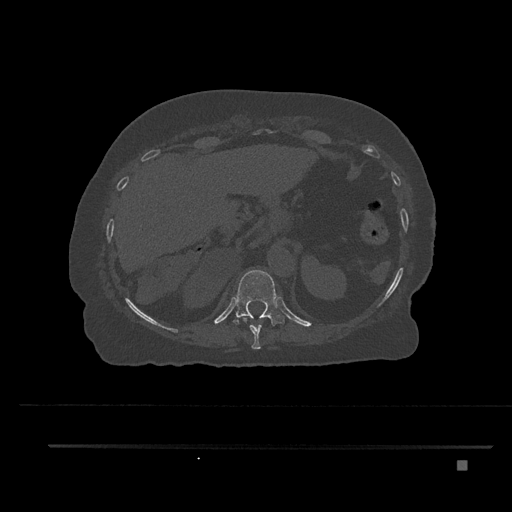
CT including the spine, one axial slice; reconstruction kernel Br40s/3; 120 kVp; bone window (W 1800 / L 400 HU); 512 × 512 image matrix, field of view 437 × 437 mm. Patient: female, 76 years. From the clinical record (not read from this slice): primary cancer: lung; vertebrae with lytic lesions (as recorded): T11, L3.
Structures marked on this image (semi-automatic segmentation, software-assisted and operator-edited):
- T10 vertebra: box from (x=242, y=318) to (x=262, y=350) px
- T11 vertebra: (x=234, y=270)–(x=285, y=326)